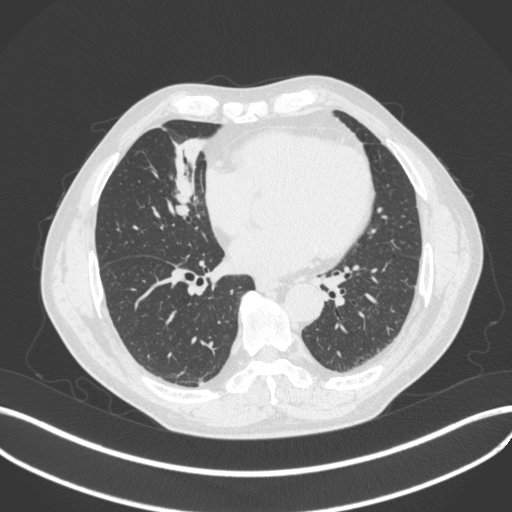
Chest CT, one axial slice. Slice 162 of 429 in the series (ordered by position). 120 kVp. Lung window (W 1500 / L -600 HU). 1 mm slice thickness. 512 × 512 image matrix. Patient: male, 61 years. From the clinical record (not read from this slice): clinical TNM (as recorded): T2b N1 M0.
Outlined on this slice (bounding box drawn by a radiologist):
- lung tumour (recorded histology: squamous cell carcinoma): box from (x=169, y=172) to (x=206, y=218) px